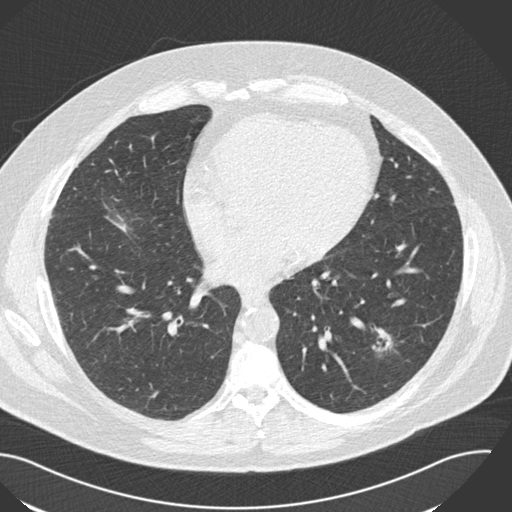
Low-dose screening chest CT, one axial slice; position 74 of 153 along the scan axis; 120 kVp; lung window (W 1500 / L -600 HU); 2 mm slice thickness; 512 × 512 image matrix, field of view 394 × 394 mm.
Annotated regions visible in this slice (outlined manually by an expert reader):
- lesion 1 (tumor, lower lobe of left lung): bounding box (x1, y1, x2, y2) in pixels: (372, 328, 392, 351)